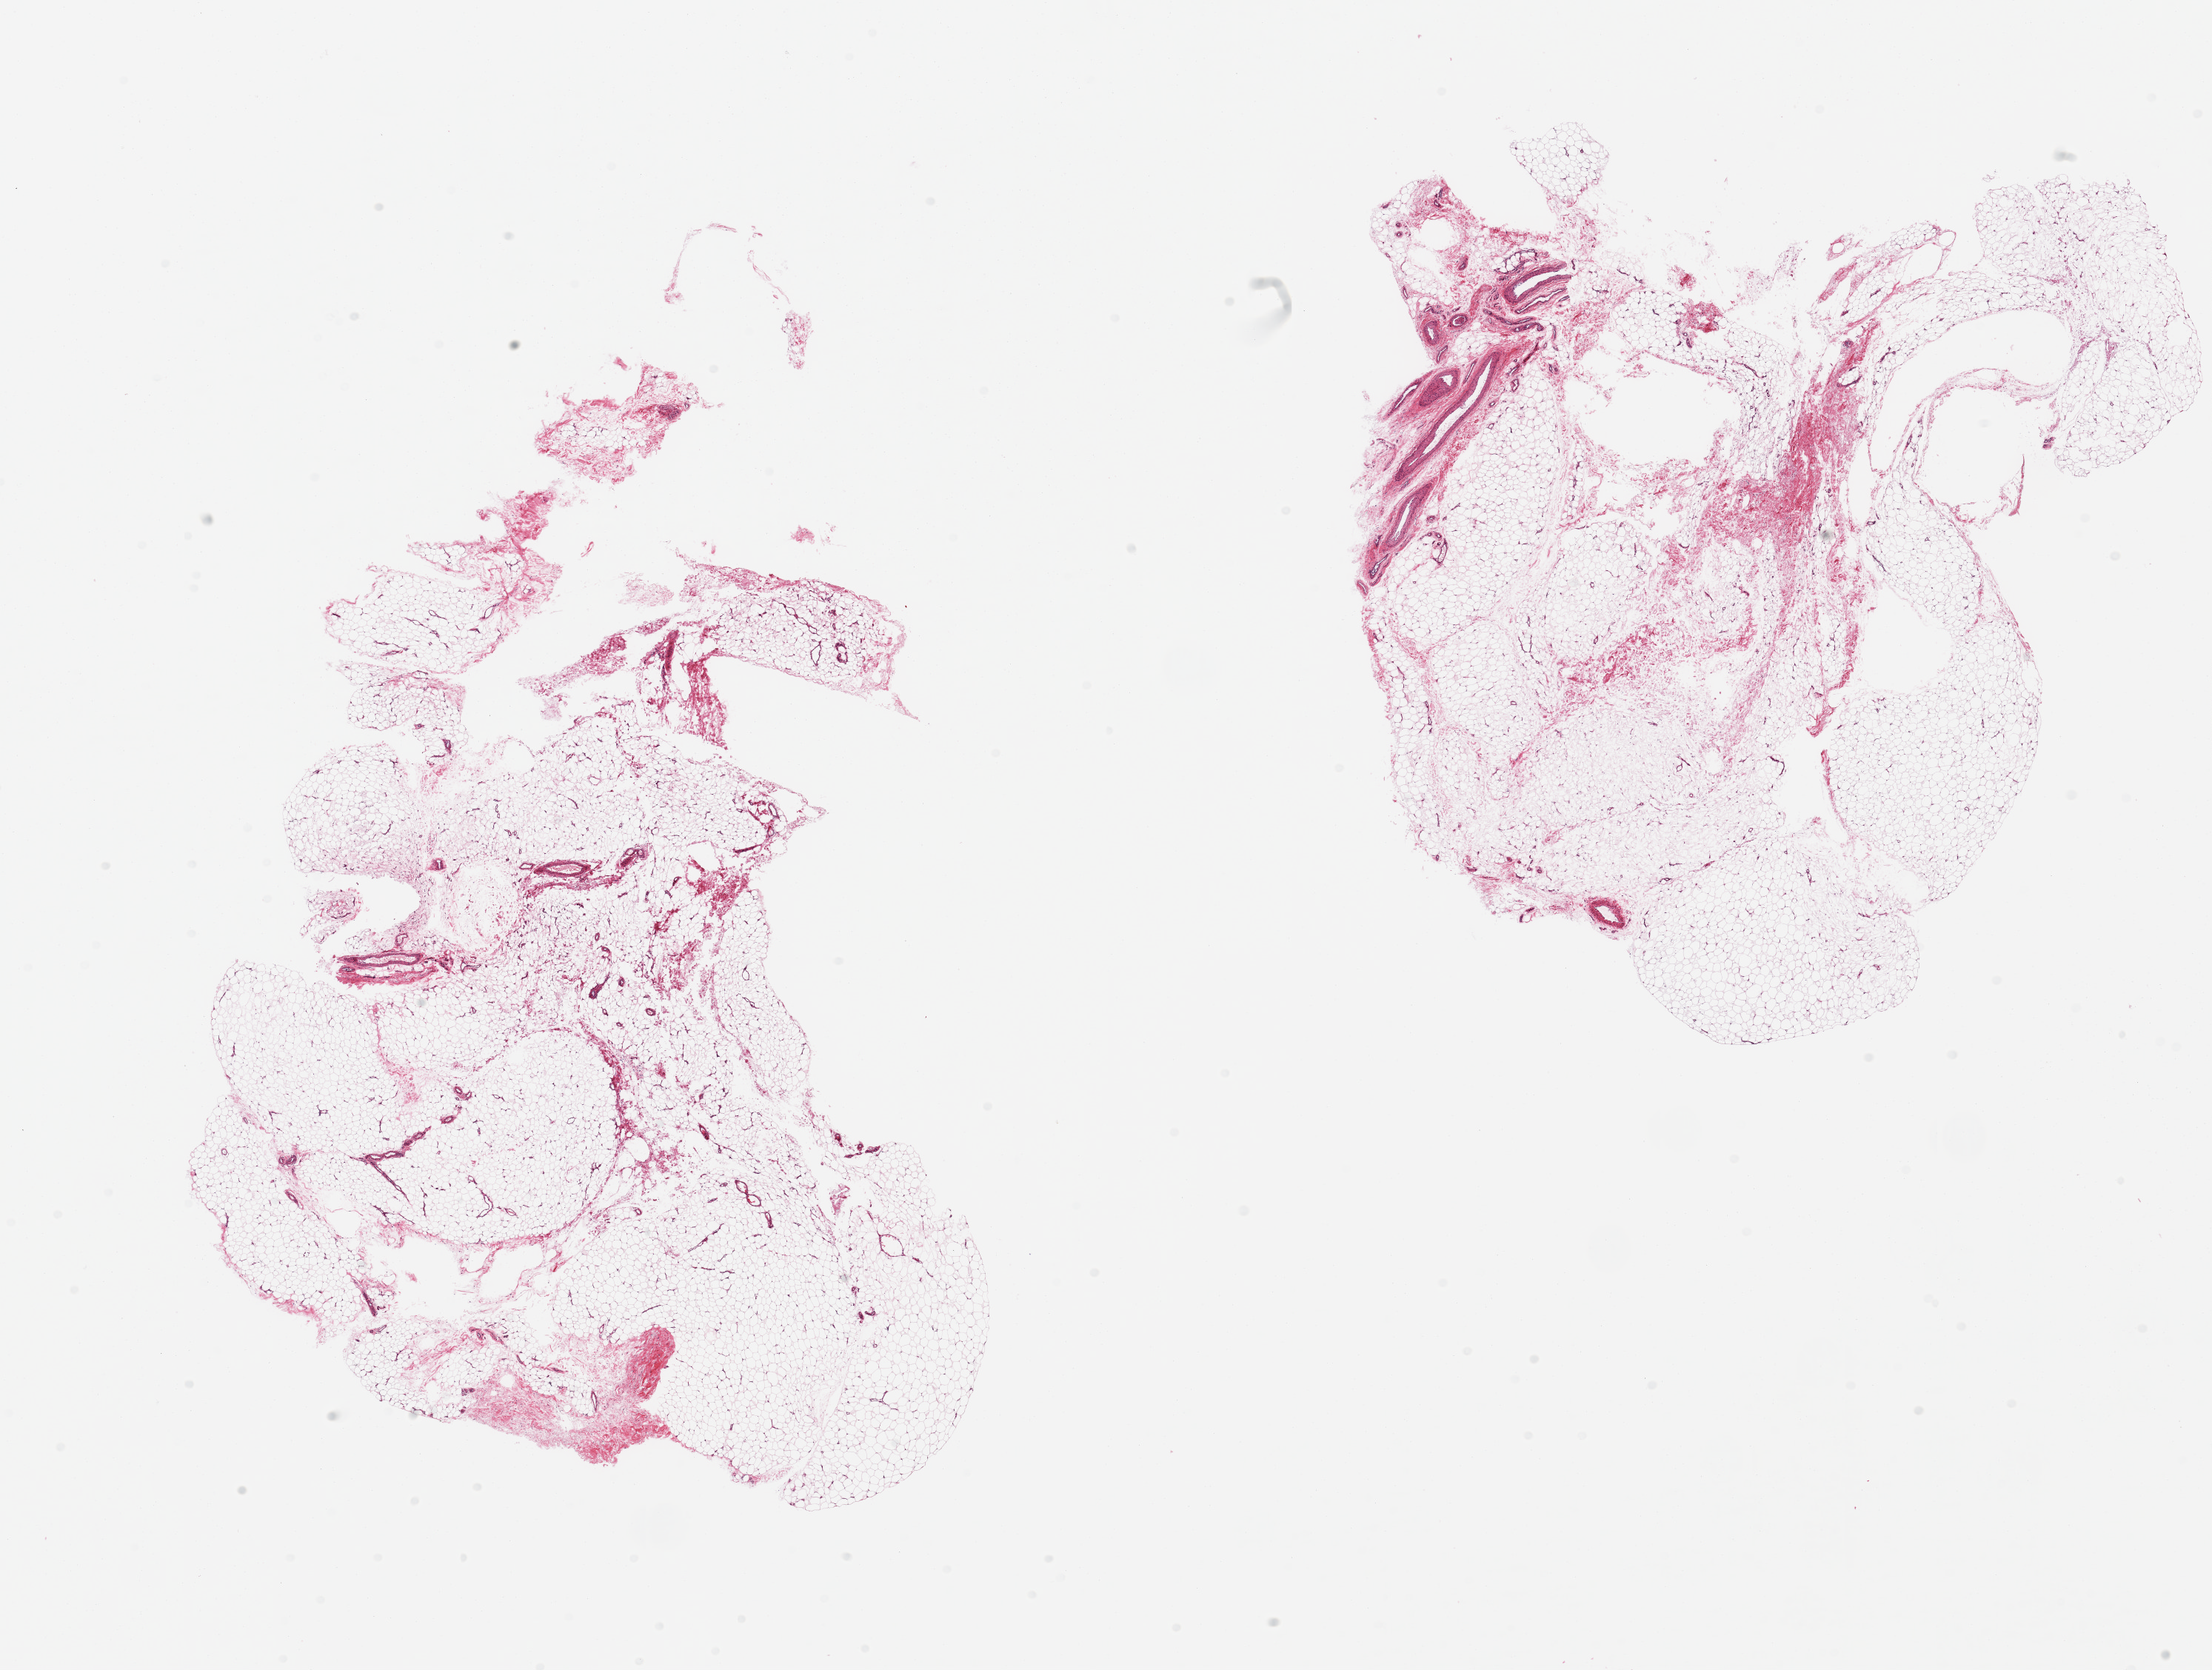
Digitized haematoxylin and eosin-stained section, brightfield — low-resolution overview of the scanned area, about 23.6 x 17.8 mm; PAXgene-fixed, paraffin-embedded tissue; target tissue: adipose tissue; tissue donor sample. Female donor.
Pathologist's review note for this sample: 2 pieces; 5 & 10% fibrovascular content.